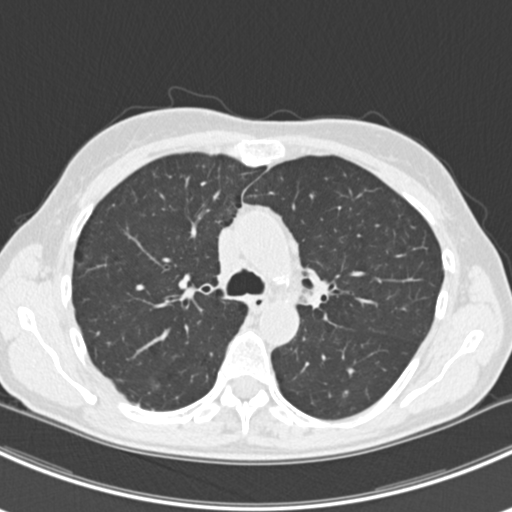
Chest CT (low-dose screening protocol), one axial image; baseline annual screen; lung window (W 1500 / L -600 HU); 2 mm slice thickness; slice 62 of 224 in the series. Female, age 63 years at enrolment. Current smoker at enrolment.
- Lesion marked by an expert reader, bounding box <134,366,176,402> (left, top, right, bottom; pixels).
- The screening reader recorded 10 non-calcified nodules or masses ≥4 mm on this exam (right lower lobe, right lower lobe, left lower lobe, left lower lobe, right middle lobe, right lower lobe, left lower lobe, left upper lobe, right upper lobe, left upper lobe); which of them this box marks is not recorded.
- Official screen result: positive, change unspecified: nodule(s) >= 4 mm or enlarging nodule(s), mass(es), or other non-specific abnormalities suspicious for lung cancer.
- Later outcome: lung cancer diagnosed 751 days after this screen (after the third annual screen) — bronchiolo-alveolar adenocarcinoma, NOS, right upper lobe, right middle lobe, right lower lobe, left upper lobe, left lower lobe, moderately differentiated (G2), stage IV (AJCC 6th edition).